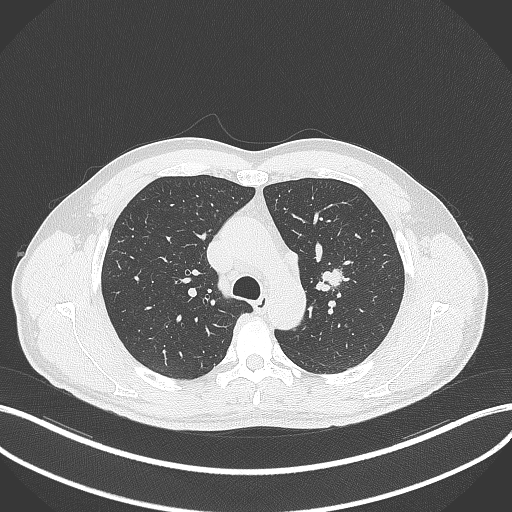
Chest CT, one axial slice. Slice 299 of 392 in the series (ordered by position). Reconstruction kernel B70f. Lung window (W 1500 / L -600 HU). 512 × 512 image matrix, field of view 400 × 400 mm. Patient: male, 50 years. From the clinical record (not read from this slice): clinical TNM (as recorded): T1c N1 M1b.
Structures marked on this image (bounding box drawn by a radiologist):
- lung tumour (recorded histology: squamous cell carcinoma): bounding box [x1, y1, x2, y2] px = [313, 266, 345, 294]